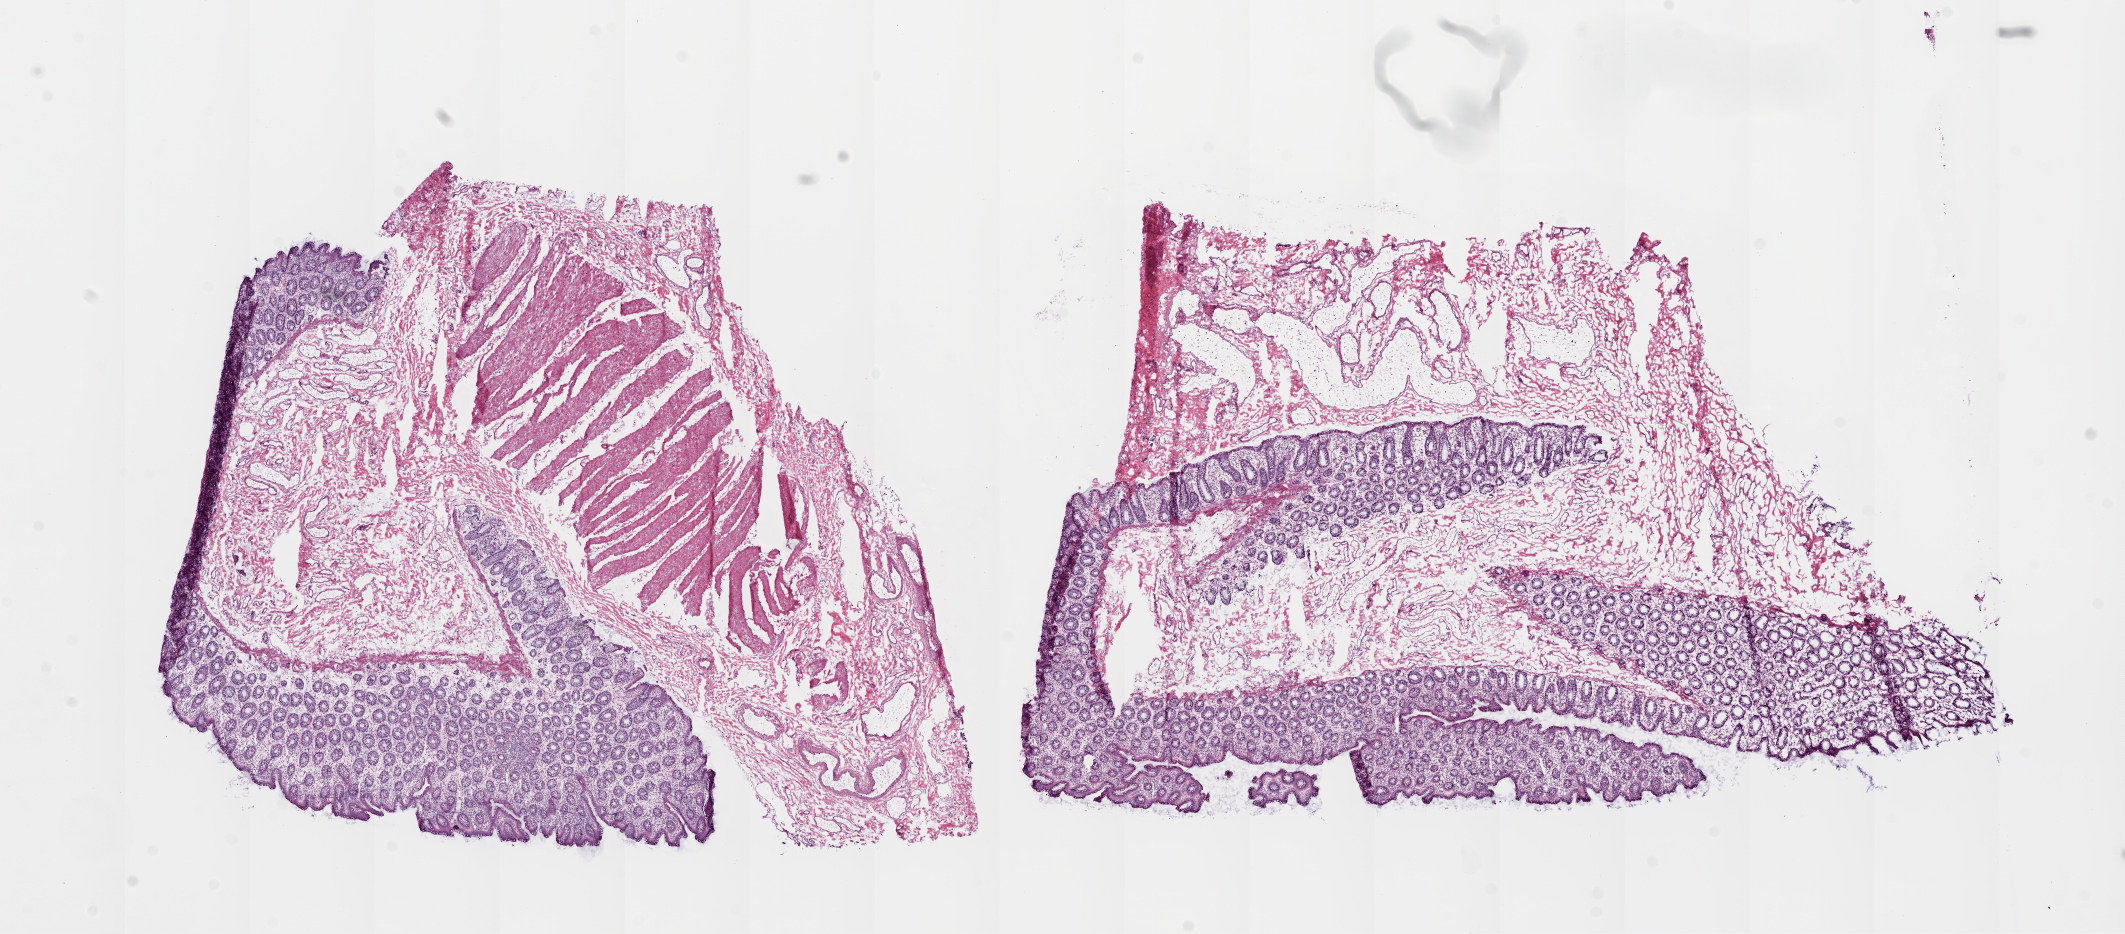
Whole-slide histology image, H&E, whole scanned area (about 17.1 x 7.5 mm, acquisition: 20x scan) shown as a low-resolution overview, frozen section from the top of the tissue portion, sample: solid tissue normal (non-tumour tissue), colon. Male patient; age at initial diagnosis 85 years.
This section: solid tissue normal sample (biorepository sample class). Patient diagnosis: Adenocarcinoma, NOS (sigmoid colon).